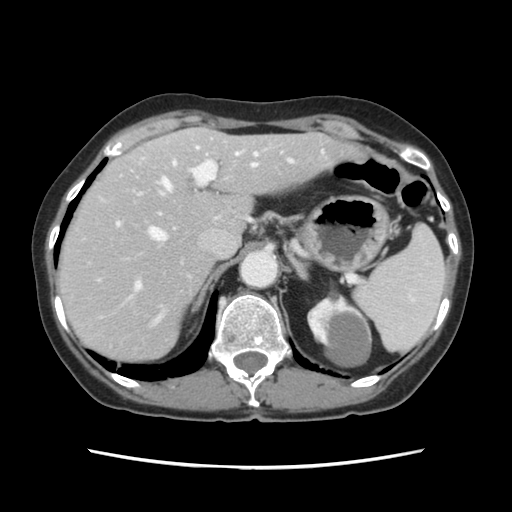
Contrast-enhanced abdominal CT, one axial slice. Position 87 of 120 along the scan axis. Intravenous contrast given. Soft-tissue window (W 400 / L 40 HU). 2.5 mm slice thickness. 512 × 512 image matrix. Female patient, age 70 years. Case-level facts recorded for this patient, not image findings: diagnosis: colorectal cancer liver metastases, imaged before liver resection; multiple liver metastases: no; largest metastasis: 2.5 cm; disease in both lobes: no.
Annotated regions visible in this slice (outlined manually by an expert reader):
- hepatic veins: bounding box [x1, y1, x2, y2] px = [149, 152, 256, 325]
- liver: [60, 129, 349, 361]
- planned liver remnant (the part of the liver to remain after resection): [112, 129, 348, 291]
- portal vein (with intrahepatic branches): [98, 147, 293, 291]